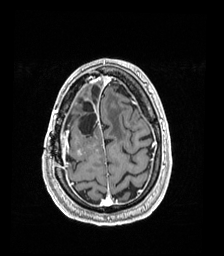
Brain MRI from a brain-tumour surgery series, one axial slice. Position 39 of 192 along the scan axis. T1-weighted post-contrast. 224 × 256 image matrix, field of view 224 × 256 mm. From the clinical record (not read from this slice): histopathology: Astrocytoma; WHO grade: 4; IDH mutation: yes.
Annotated regions visible in this slice (outlined manually by an expert reader):
- previous resection cavity: bounding box <79,102,97,135> (left, top, right, bottom; pixels)
- tumour: <77,149,83,156>